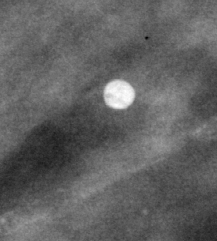
Crop from a digitized film mammogram around one marked abnormality, right breast, MLO view, BI-RADS breast density category 2 (scale 1–4).
Marked abnormality: calcifications, morphology lucent center; BI-RADS assessment category 2; subtlety rating 4 on a 1 (subtle) to 5 (obvious) scale; benign without callback (not worked up further).